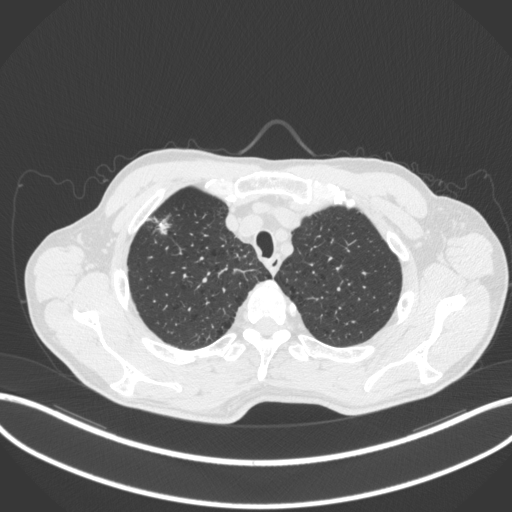
Chest CT, one axial slice. Slice 358 of 414 in the series (ordered by position). Lung window (W 1500 / L -600 HU). 1 mm slice thickness. 512 × 512 image matrix, field of view 400 × 400 mm. Patient: male, 69 years. From the clinical record (not read from this slice): clinical TNM (as recorded): T1b N1 M0.
Structures marked on this image (bounding box drawn by a radiologist):
- lung tumour (recorded histology: adenocarcinoma): box from (x=151, y=214) to (x=173, y=238) px